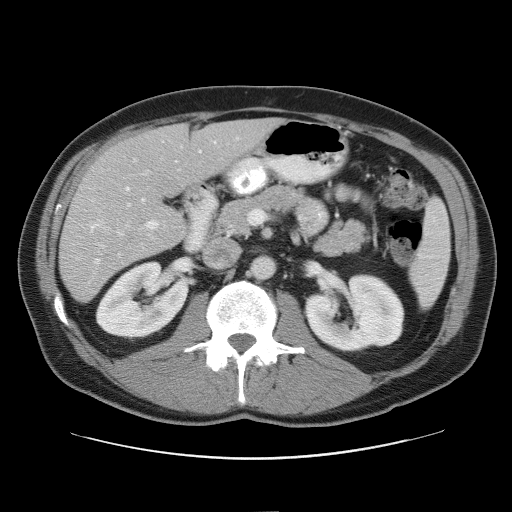
Contrast-enhanced abdominal CT, one axial slice; 120 kVp; intravenous contrast given; soft-tissue window (W 400 / L 40 HU); 5 mm slice thickness; 512 × 512 image matrix, field of view 393 × 393 mm. Male patient, age 70 years. Case-level facts recorded for this patient, not image findings: diagnosis: colorectal cancer liver metastases, imaged before liver resection; multiple liver metastases: yes; largest metastasis: 4 cm; chemotherapy before resection: yes.
Structures marked on this image (outlined manually by an expert reader):
- hepatic veins: bounding box (x1, y1, x2, y2) in pixels: (81, 171, 154, 266)
- liver: (60, 119, 277, 302)
- planned liver remnant (the part of the liver to remain after resection): (116, 119, 278, 195)
- portal vein (with intrahepatic branches): (125, 141, 217, 230)